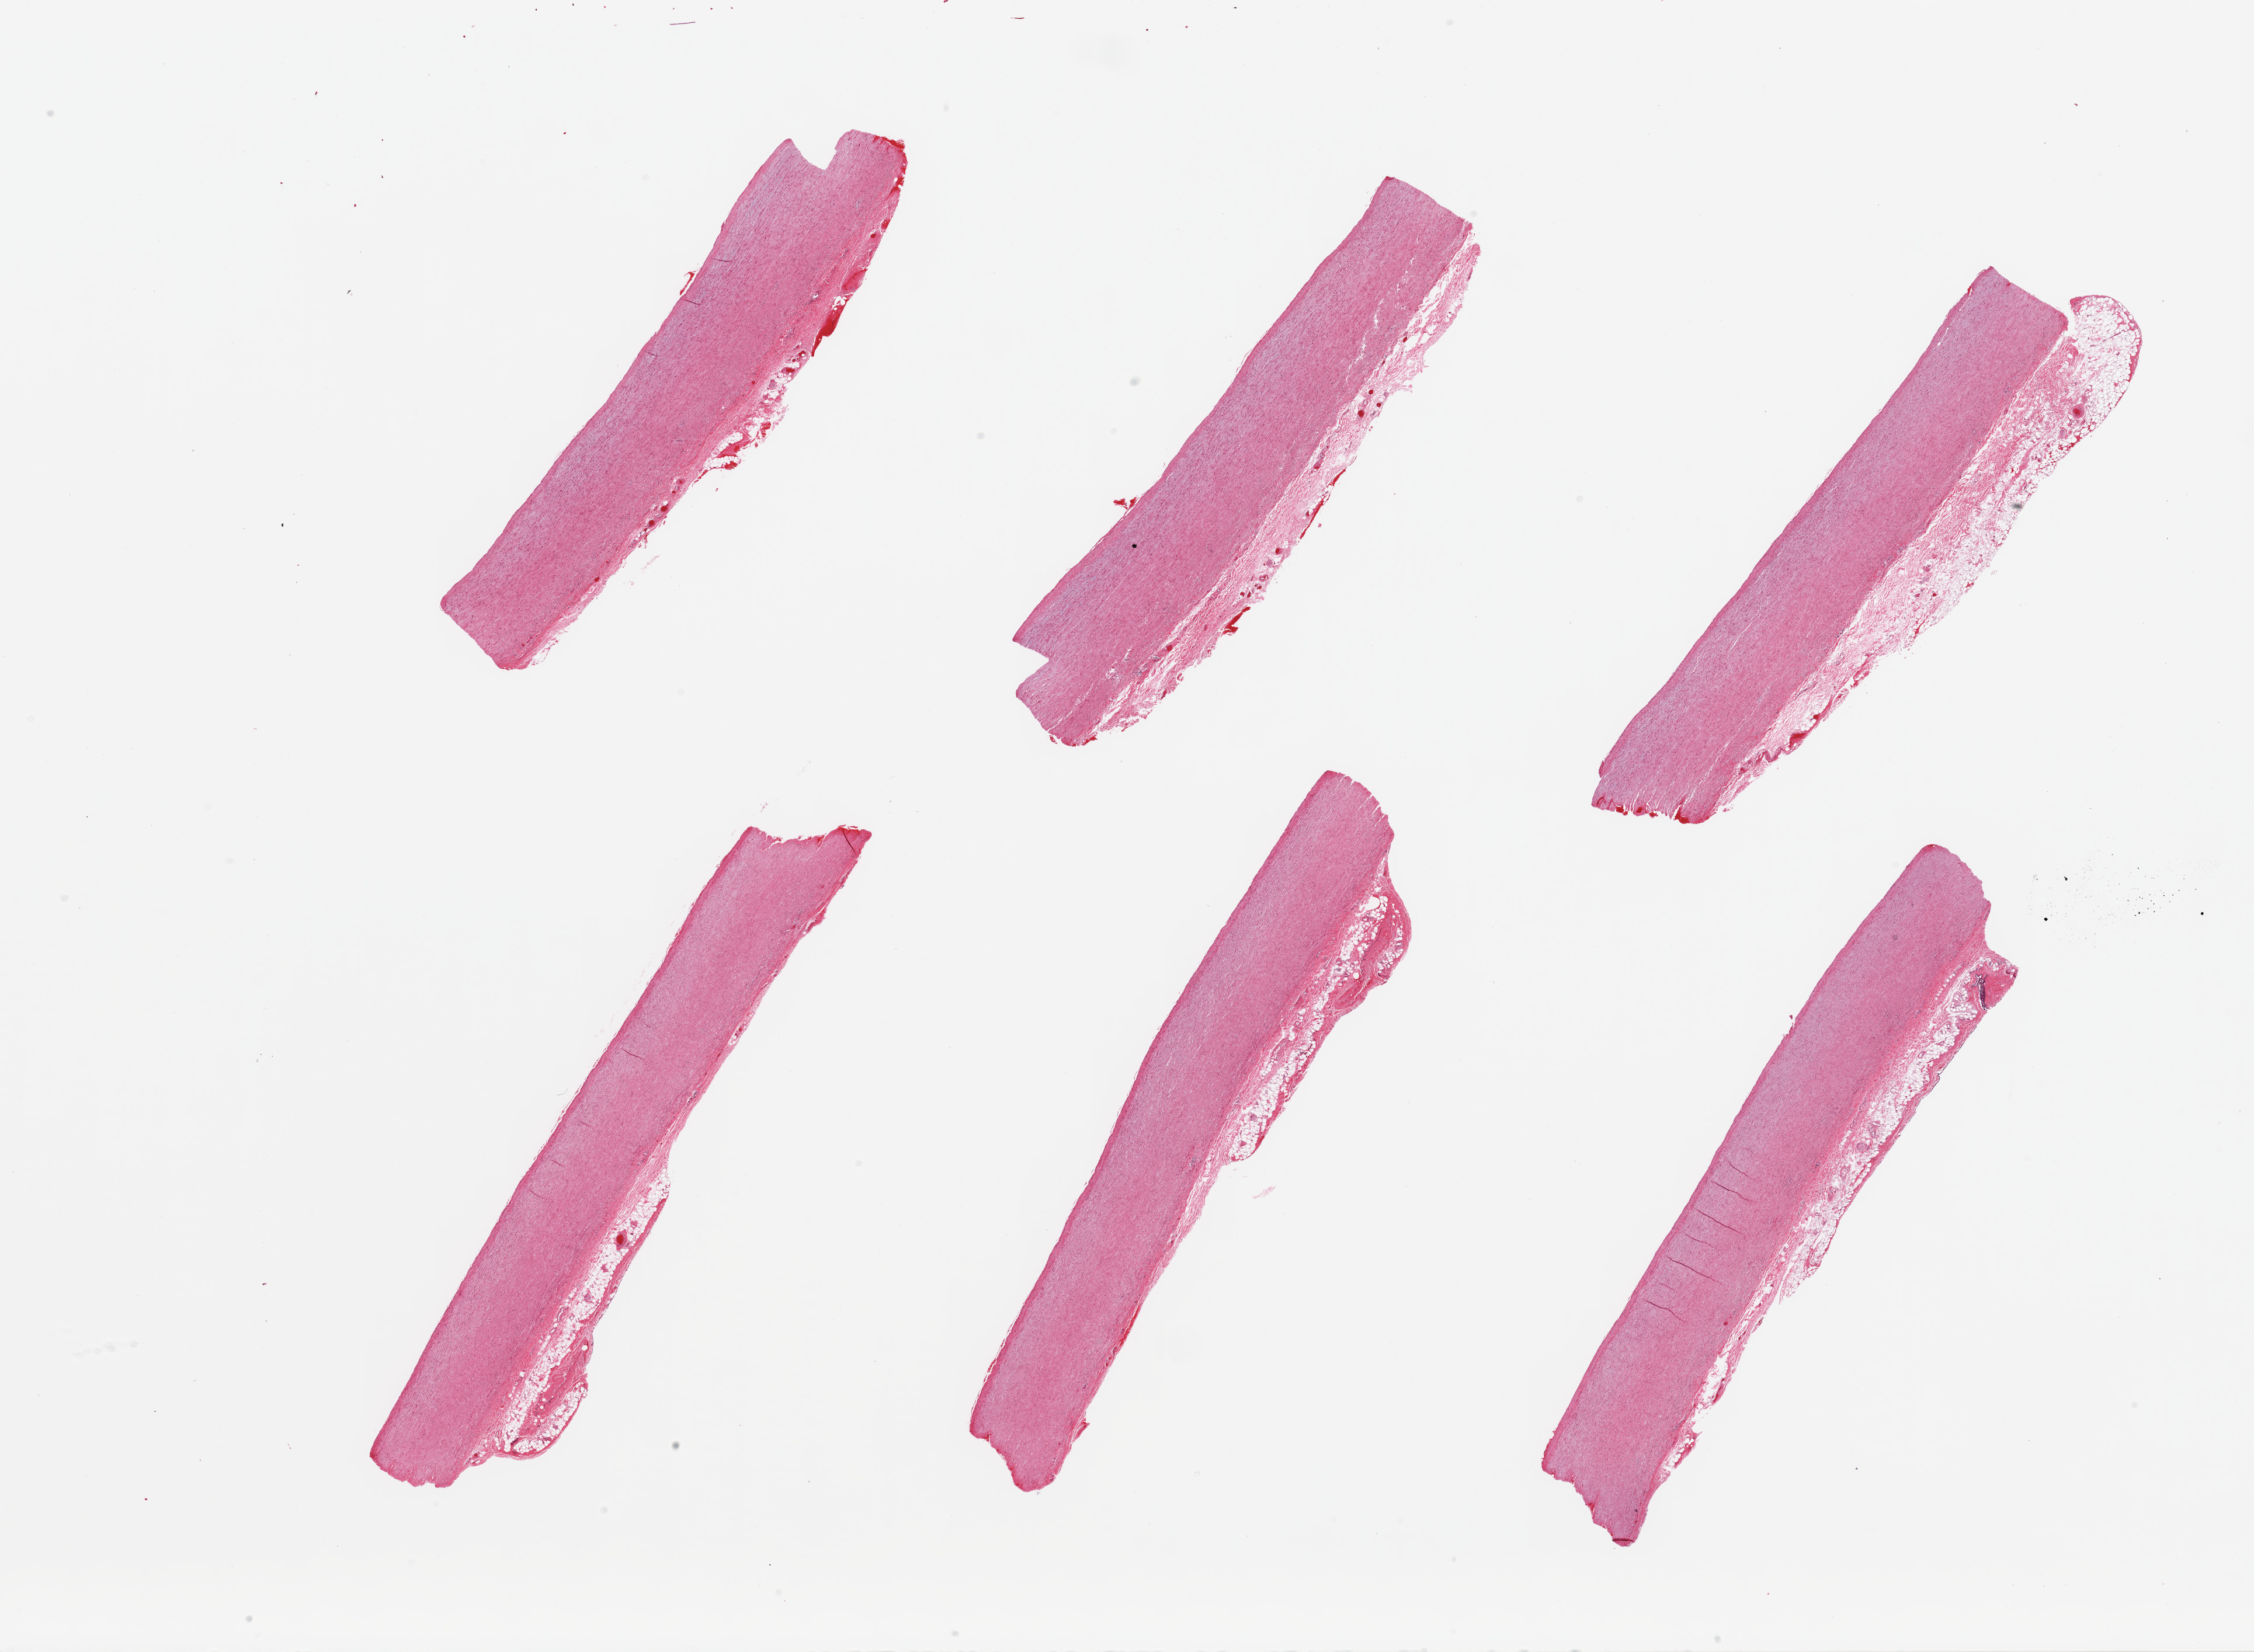
Digitized hematoxylin and eosin (H&E)-stained section, whole scanned area (about 30.5 x 22.4 mm) shown as a low-resolution overview. PAXgene-fixed paraffin-embedded (PFPE) section. Sampled site (target tissue): aorta. Tissue donor sample. Female donor.
• pathologist's review note for this sample: 6 pieces, layer of adherent serosa/fat up to ~1mm